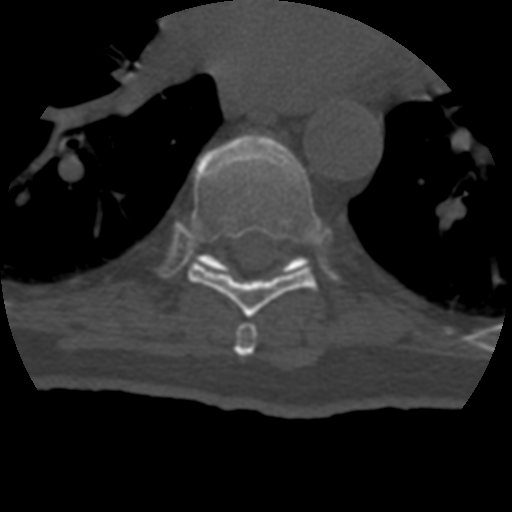
CT including the spine, one axial slice. Slice 255 of 399 in the series (ordered by position). Bone window (W 1800 / L 400 HU). 1.25 mm slice thickness. 512 × 512 image matrix, field of view 160 × 160 mm. Patient age 69 years. From the clinical record (not read from this slice): primary cancer: prostate.
Annotated regions visible in this slice (semi-automatic segmentation, software-assisted and operator-edited):
- T7 vertebra: bounding box <234,323,257,357> (left, top, right, bottom; pixels)
- T8 vertebra: <188,135,320,317>
- T9 vertebra: <200,253,305,268>